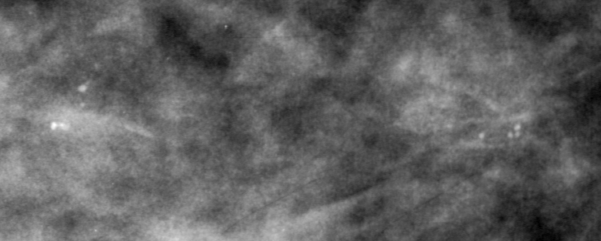
Region of interest cut from a scanned film mammogram (one marked finding), left breast, CC view.
- Finding: calcifications, morphology pleomorphic, distribution segmental; BI-RADS assessment category 4; subtlety rating 2 on a 1 (subtle) to 5 (obvious) scale; pathology (as recorded): malignant.